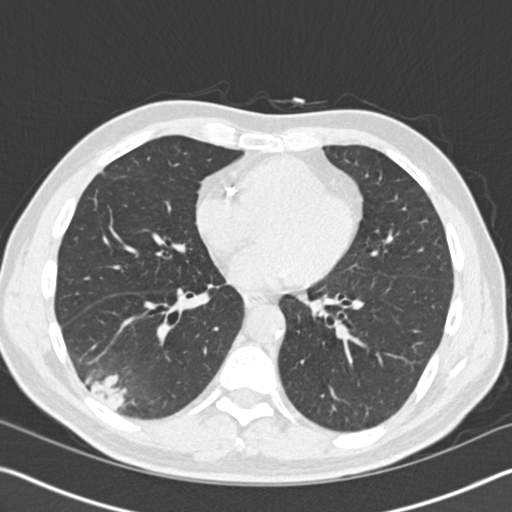
Low-dose screening chest CT, axial slice; baseline screening round; lung window (W 1500 / L -600 HU); standard (soft-tissue) reconstruction kernel (B30f); slice 92 of 161 in the series; 512 × 512 image matrix. Male participant, aged 61 years at enrolment. Current smoker at enrolment.
- Lesion marked by an expert reader, bounding box (x1, y1, x2, y2) in pixels: (51, 331, 159, 425).
- Screening reader's record for this exam (one nodule recorded; not confirmed to be the boxed lesion): non-calcified nodule or mass ≥4 mm, right lower lobe, 52 × 36 mm, spiculated (stellate) margins, soft tissue attenuation.
- Official screen result: positive, change unspecified: nodule(s) >= 4 mm or enlarging nodule(s), mass(es), or other non-specific abnormalities suspicious for lung cancer.
- Lung cancer was diagnosed 392 days after this screen (after the second annual screen): bronchiolo-alveolar adenocarcinoma, NOS, right lower lobe, moderately differentiated (G2), stage IIIB (AJCC 6th edition), 90 mm at pathology.